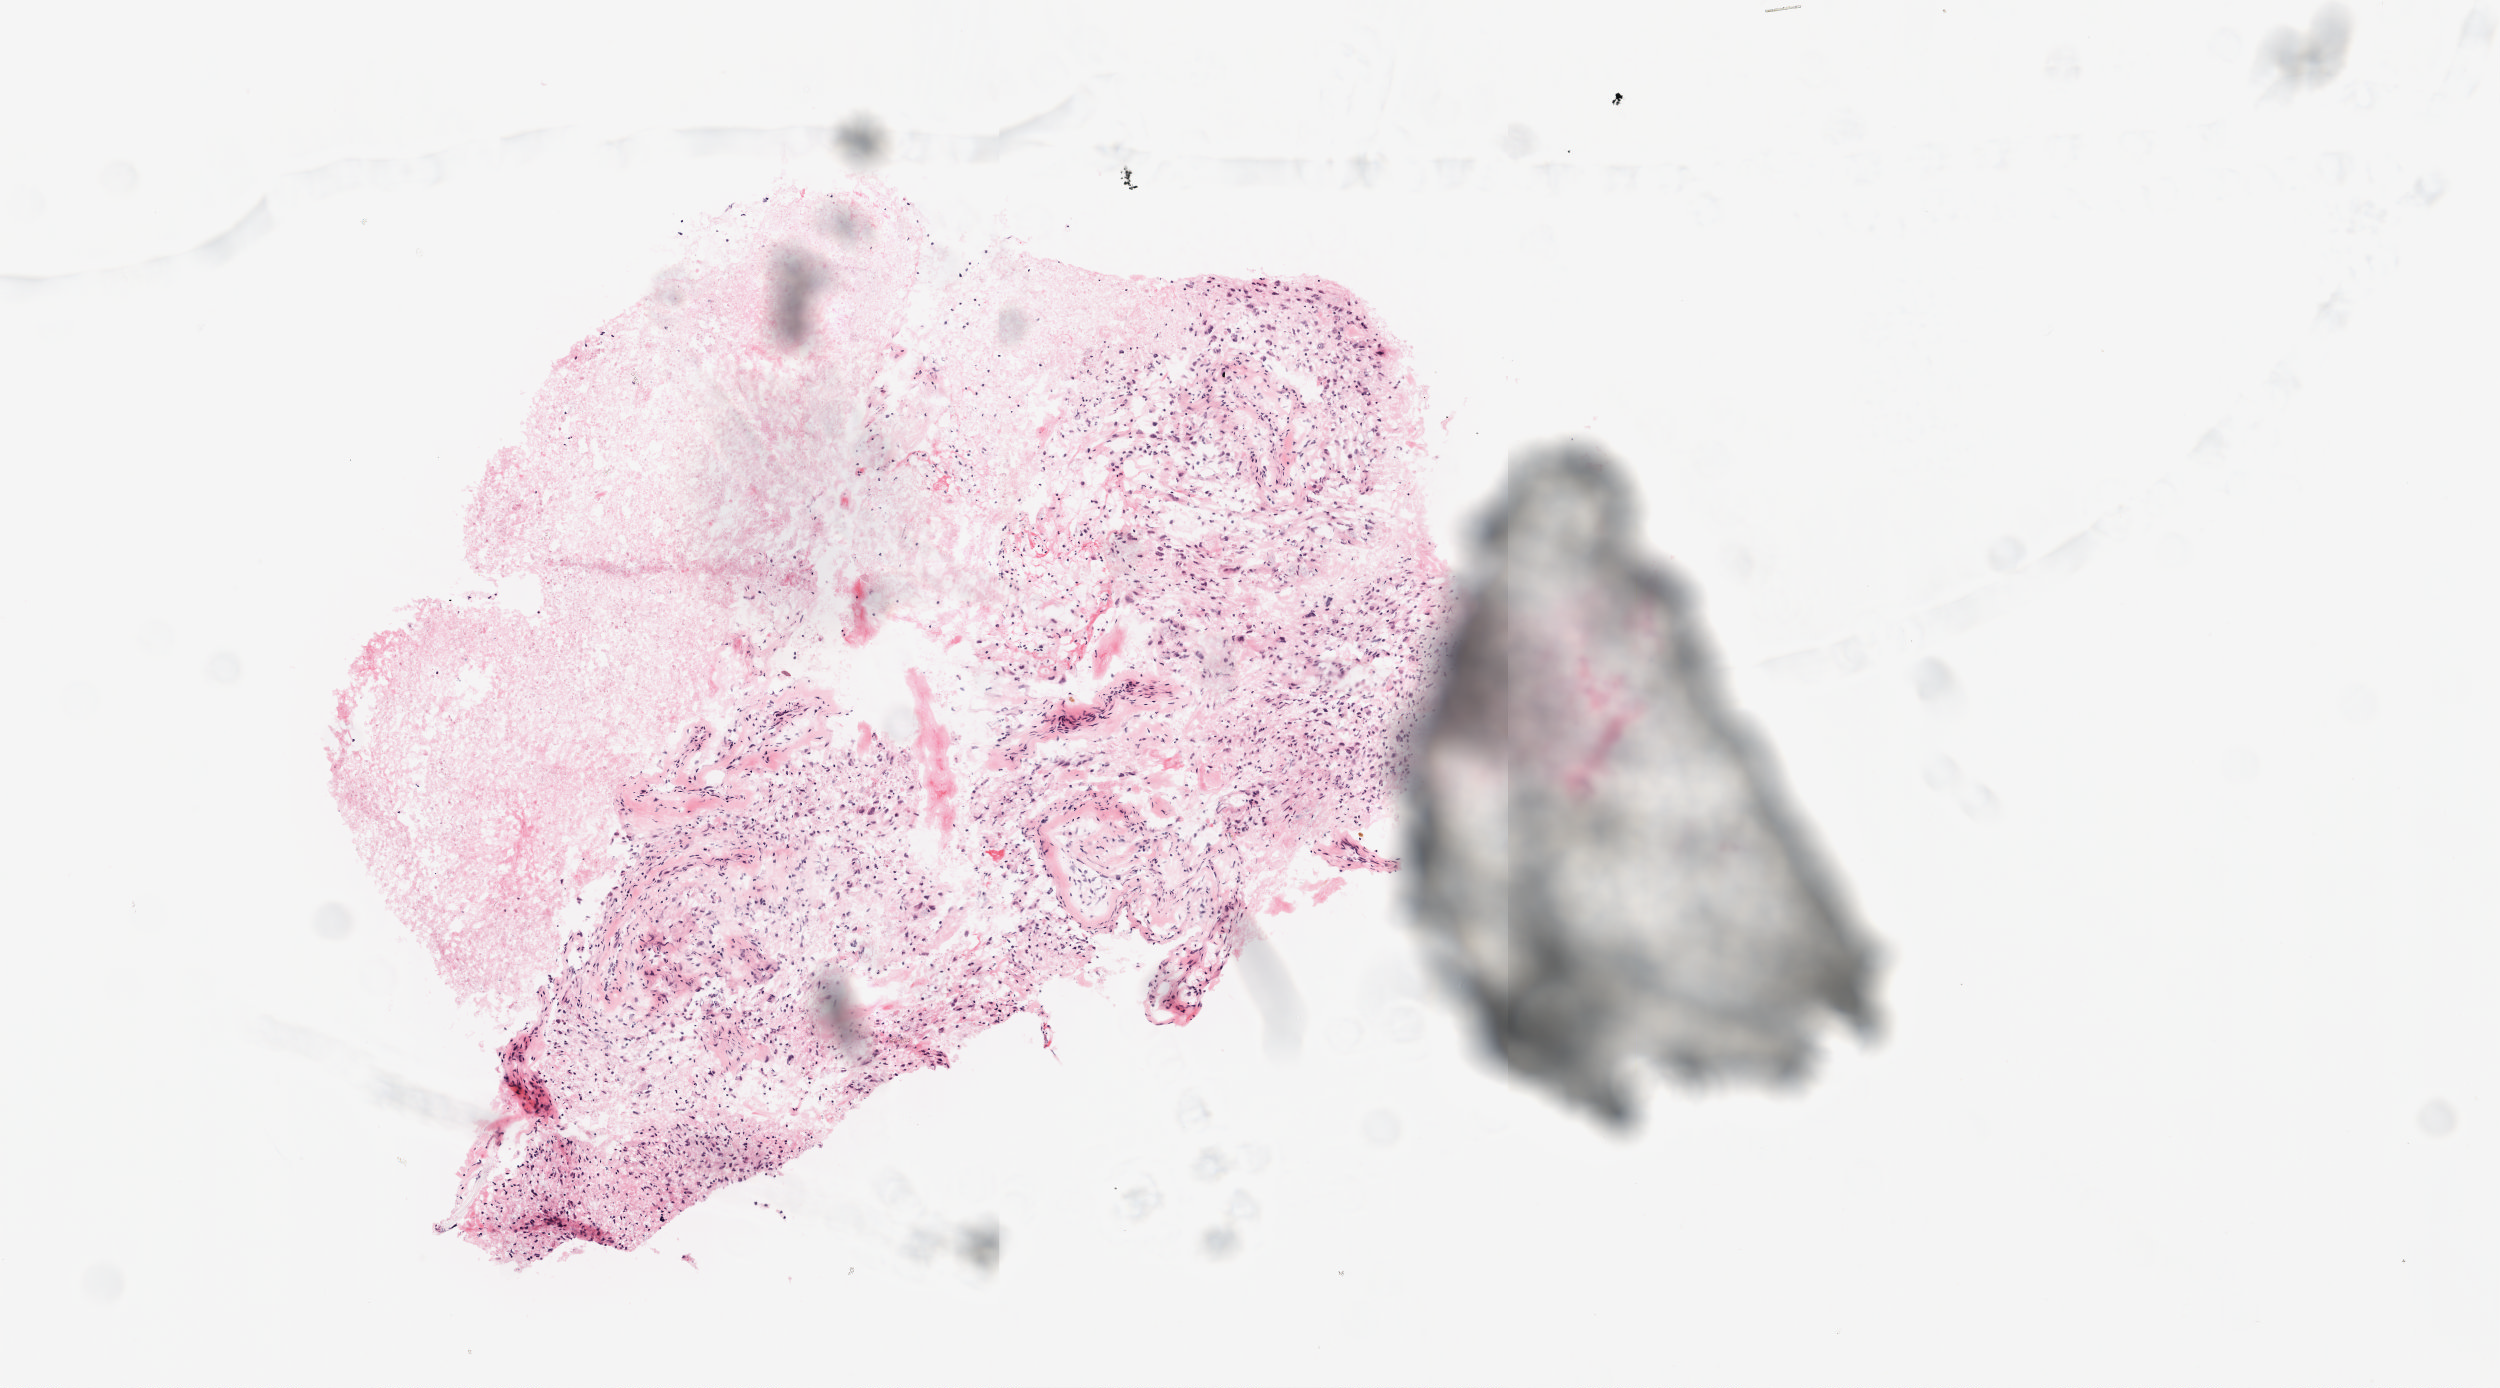
H&E whole-slide image — shown as a low-resolution overview of the whole scanned area (about 5.0 x 2.8 mm). Frozen section from the top of the tissue portion. Sample: primary tumour, brain. Male patient; age at initial diagnosis 81 years. Slide review estimates, as recorded: tumour cells 50%, tumour nuclei 100%, normal cells 0%, stromal cells 50%, necrosis 0%.
Diagnosis: Glioblastoma.